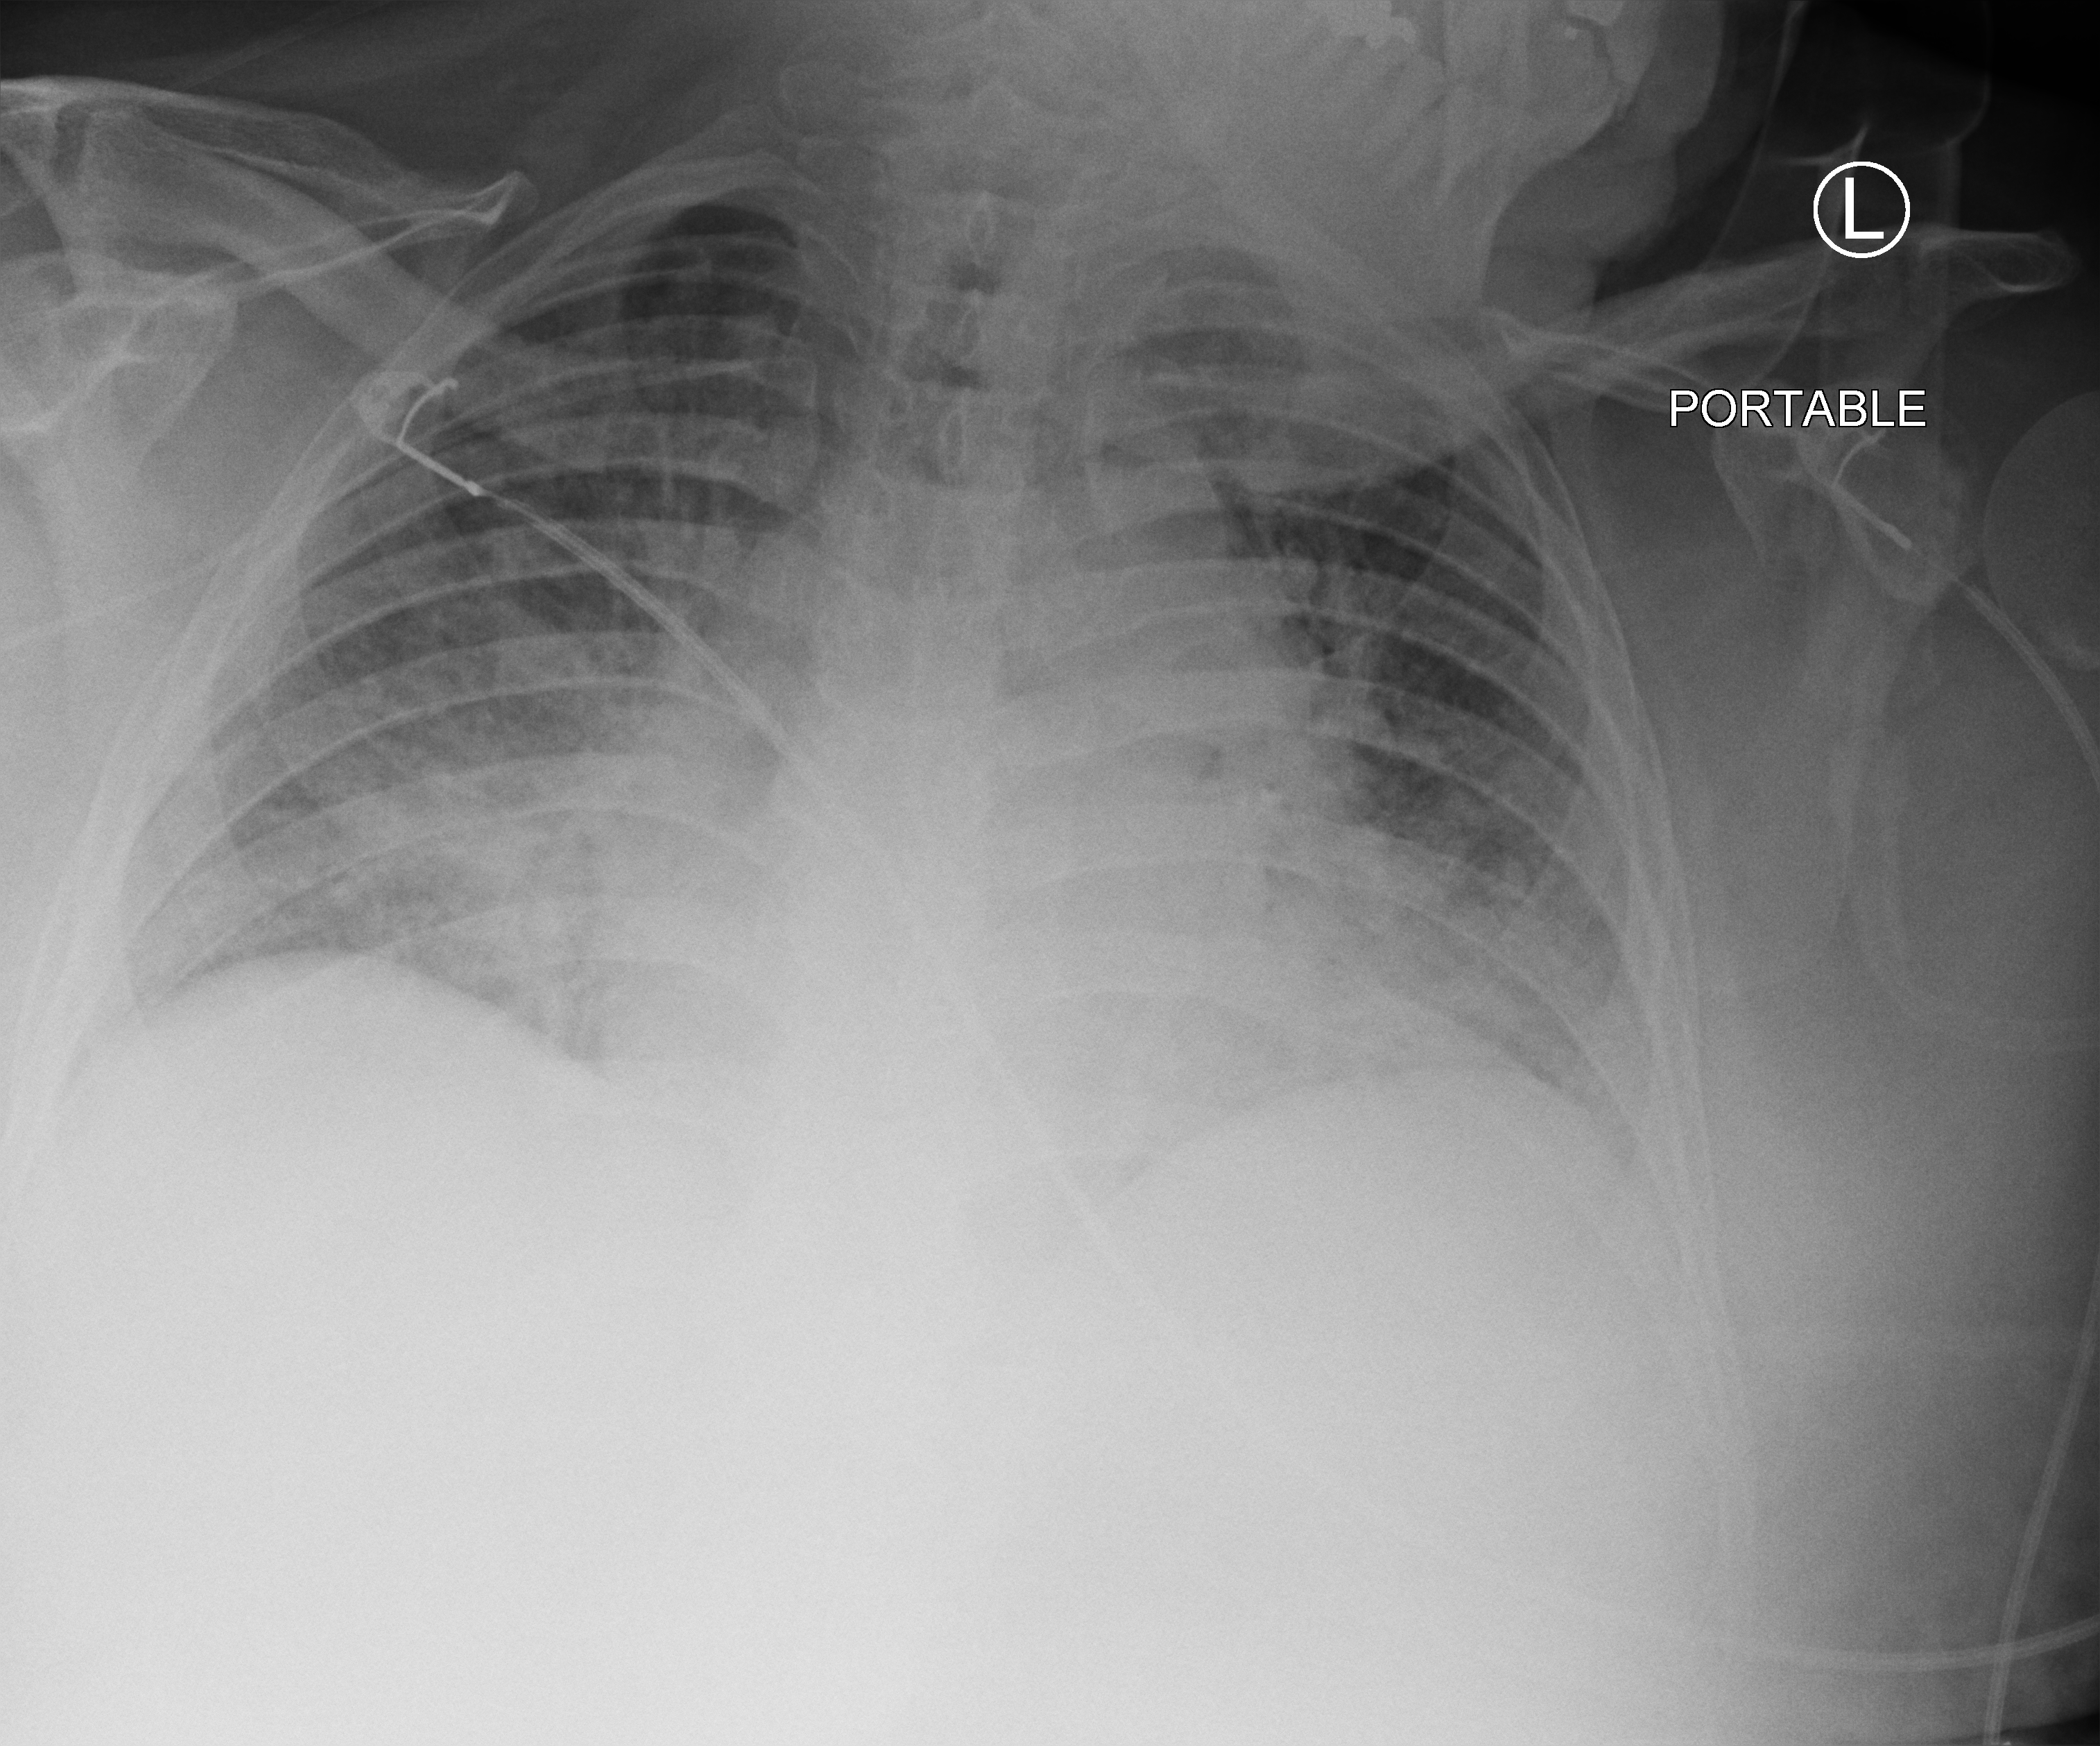
Chest X-ray (portable). Patient hospitalised with COVID-19; male, aged 18–59 years.
Hospital-stay facts (about this admission, not read from this image; timing relative to this image not recorded):
- length of hospital stay: 28 days
- other chronic lung disease (admission record): no